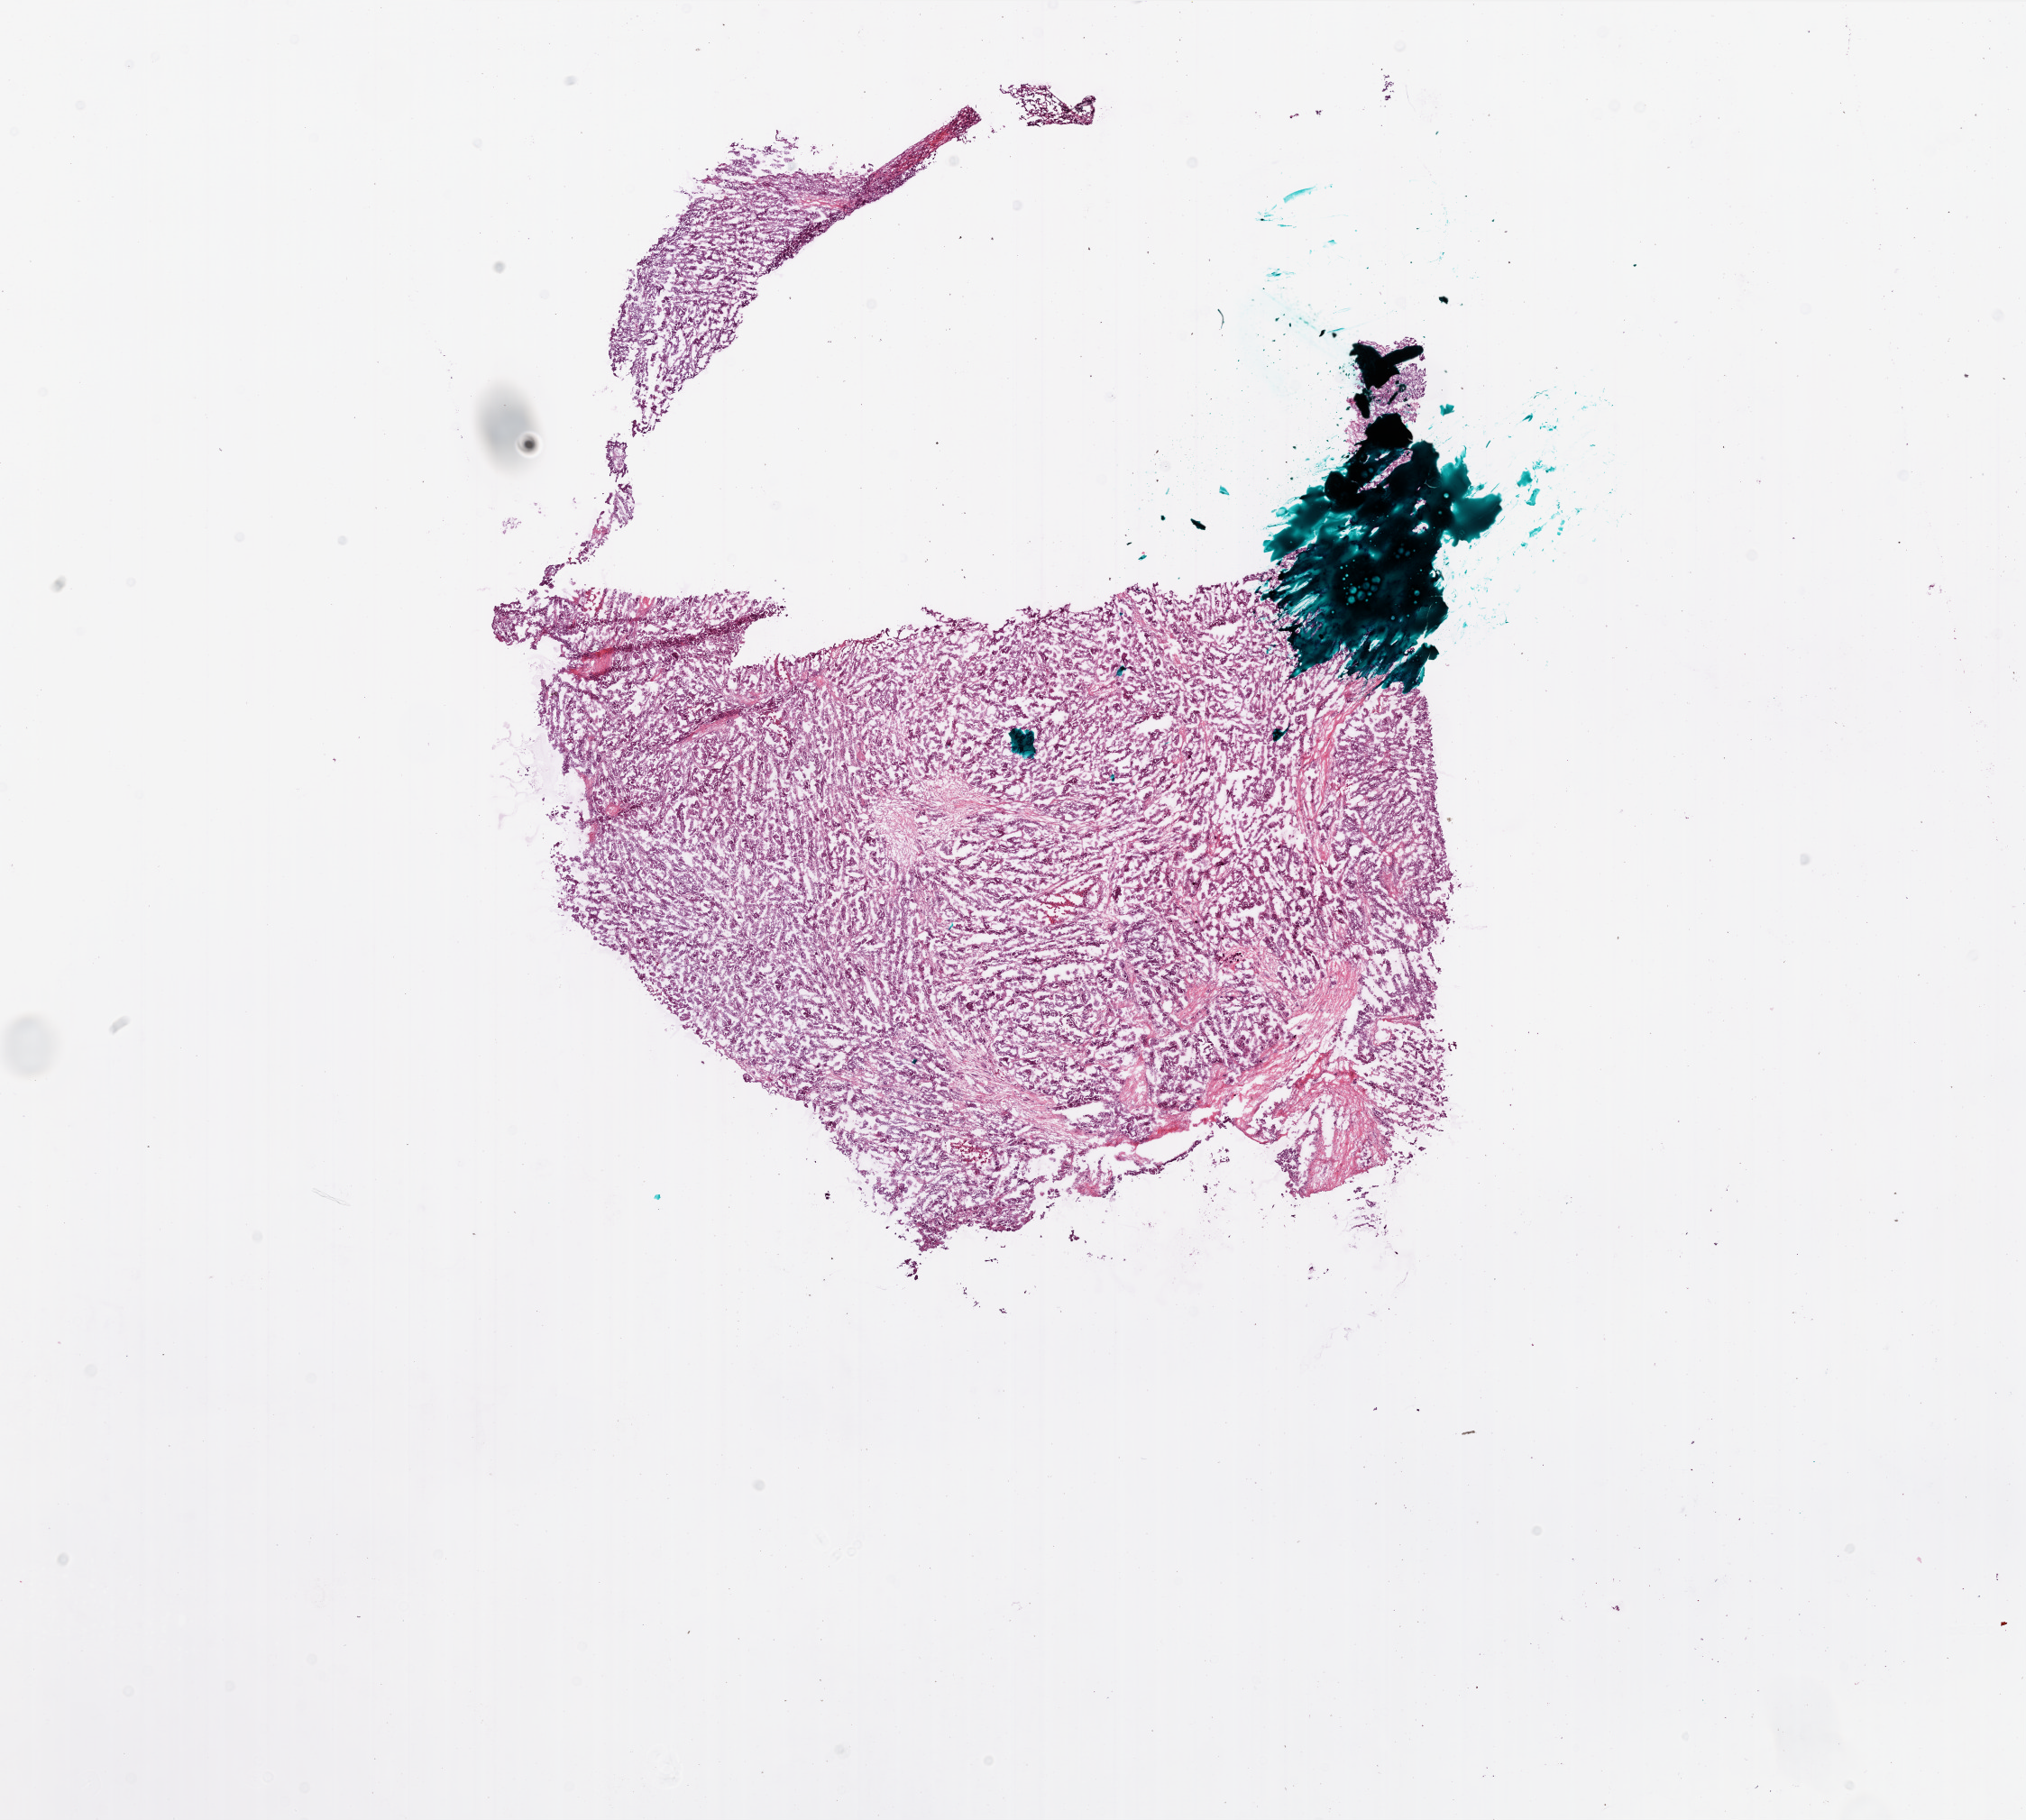
Digitized H&E tissue section (whole slide), whole scanned area (about 18.0 x 16.2 mm, from a 20x scan) shown as a low-resolution overview, frozen section from the bottom of the tissue portion, primary tumour sample from the ovary. Female, age 54 years at initial diagnosis. Histologic grade: G3 (poorly differentiated). Pathologist review of this section (percent, as recorded): tumour cells 88%, tumour nuclei 90%, normal cells 10%, stromal cells 0%, necrosis 2%.
* FIGO stage: IIIC
* diagnosis: Serous cystadenocarcinoma, NOS